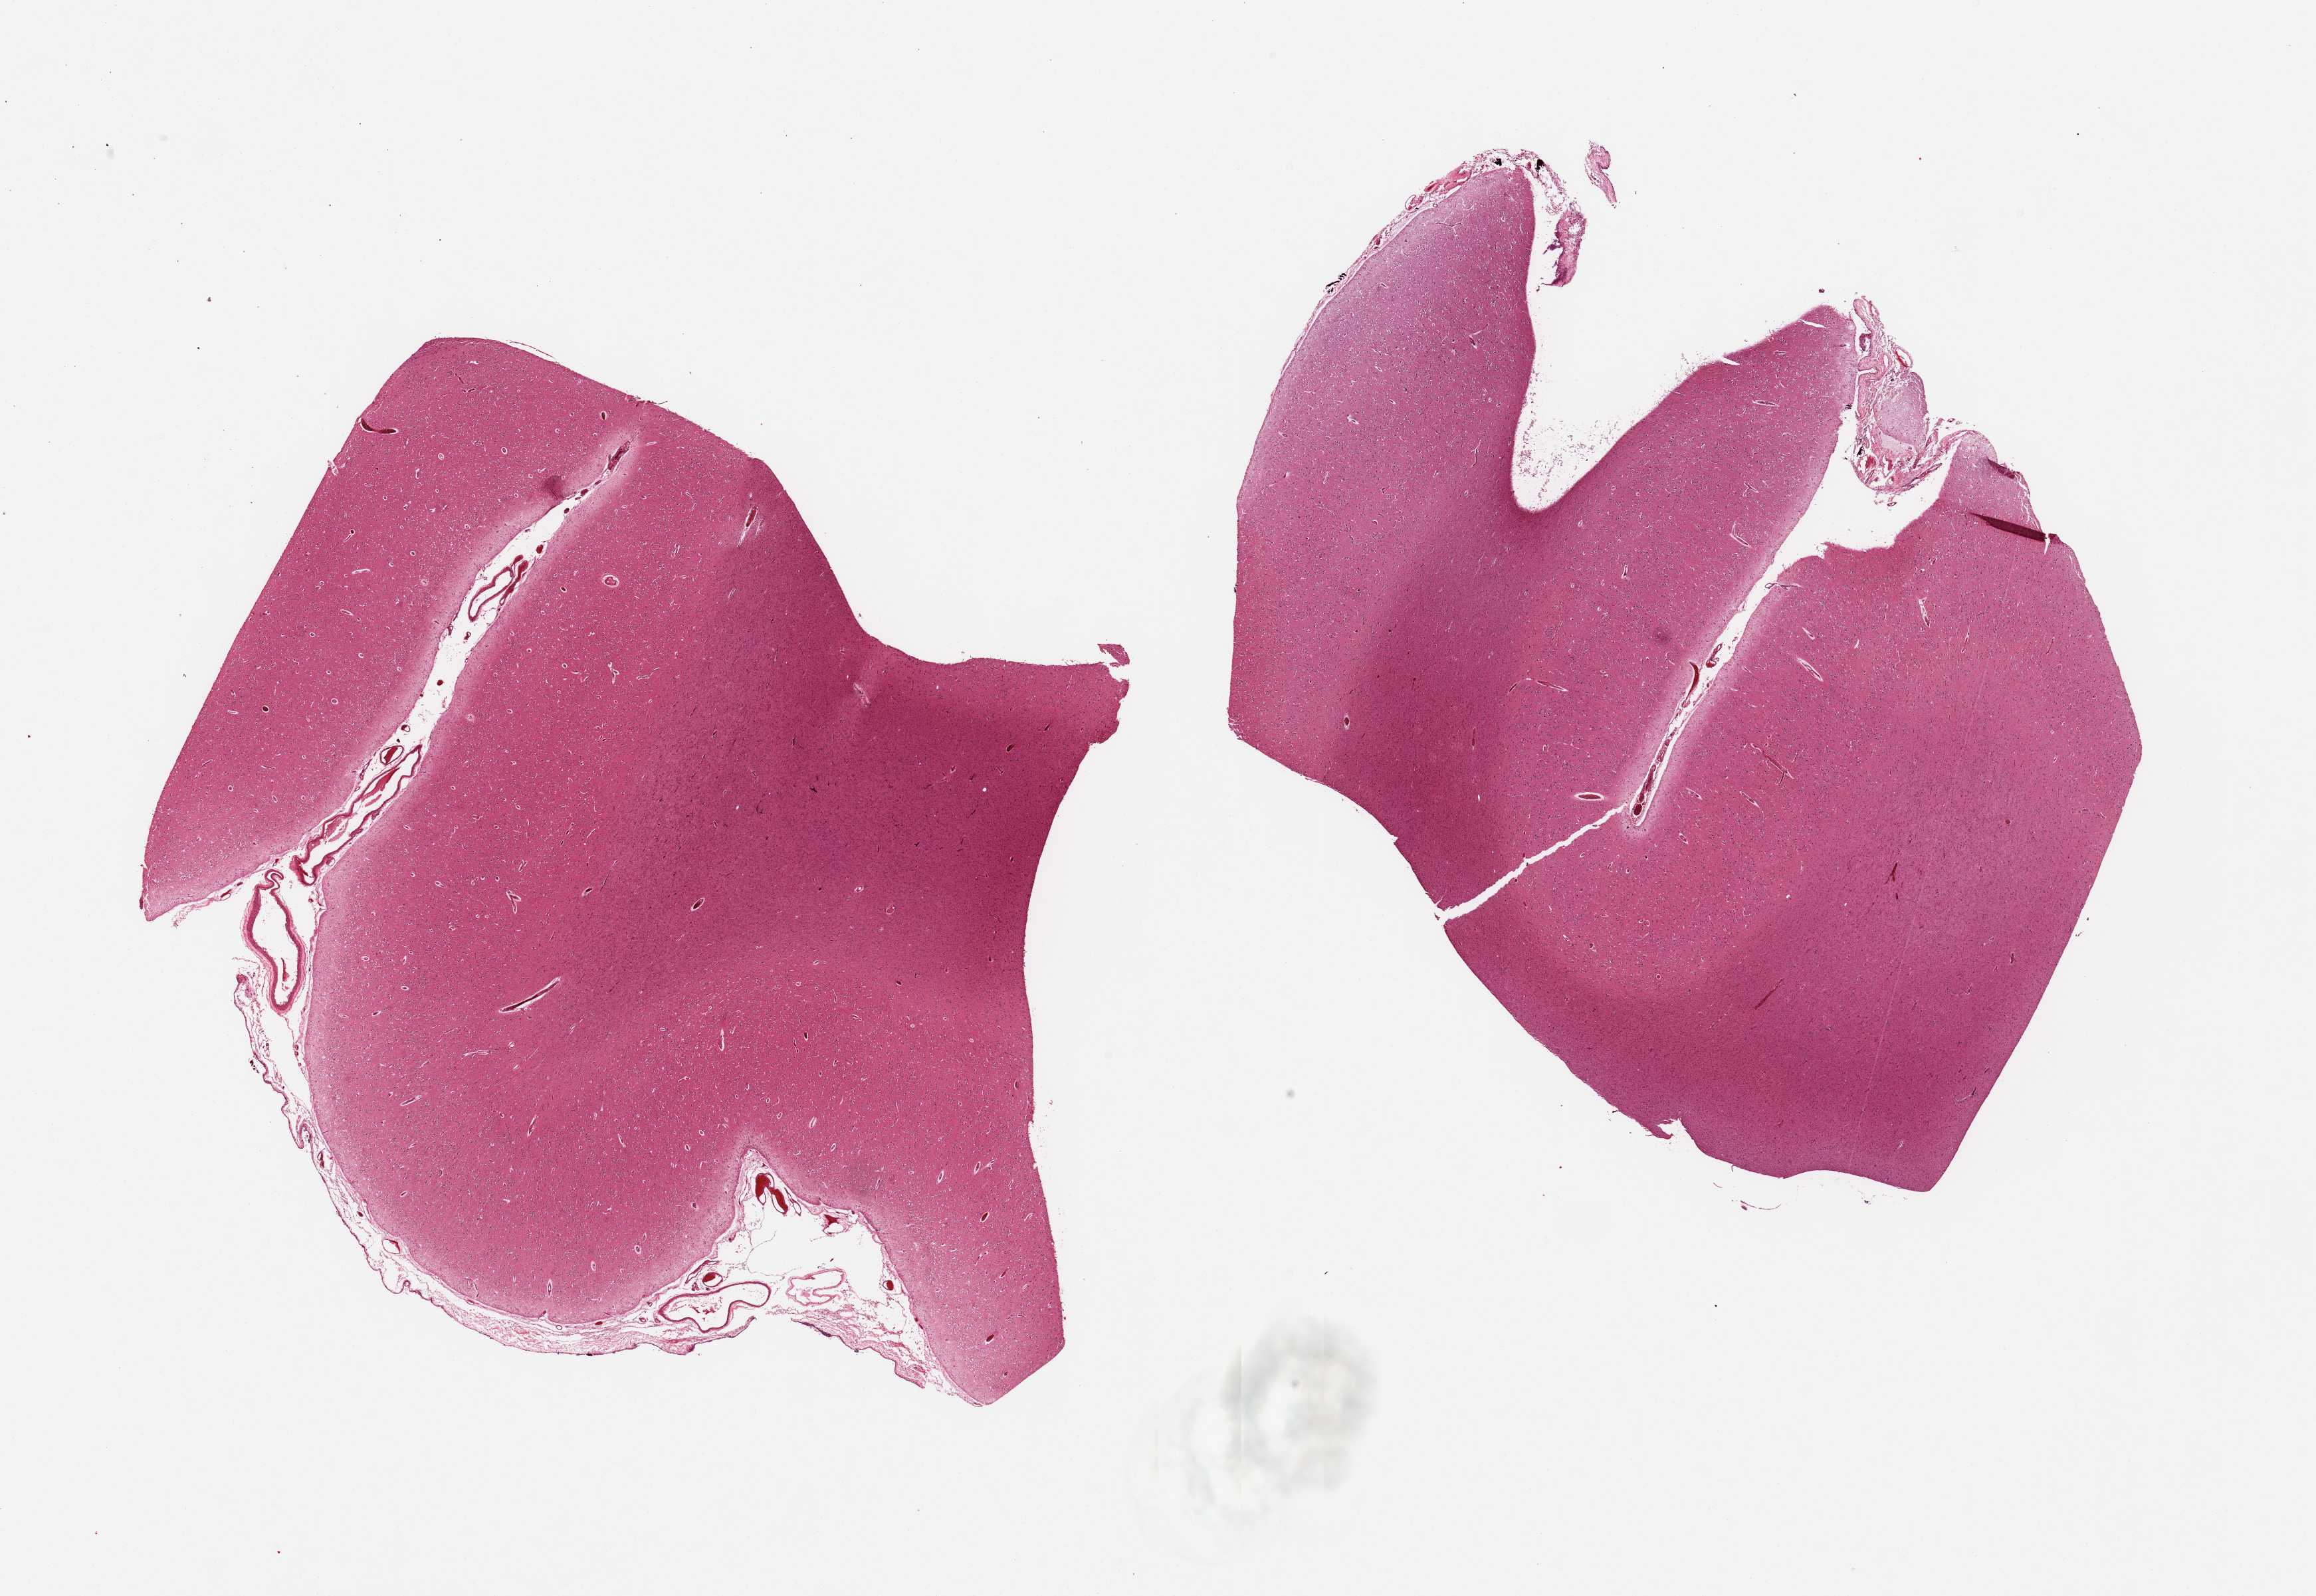
Haematoxylin and eosin whole-slide image — a low-resolution overview of the entire scanned area, about 27.6 x 19.0 mm; PAXgene-fixed, paraffin-embedded tissue; section of cerebral cortex (target tissue); donor tissue sample. Donor: male.
• reviewer comment on this tissue sample: 2 pieces, no abnormalities